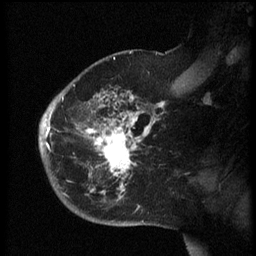
Breast MRI (dynamic contrast-enhanced), one sagittal slice; slice 42 of 60 in the series (ordered by position); dynamic contrast-enhanced series, image 2 of 3 at this slice position (ordered by acquisition); 1.5 T; TE 4.2 ms, TR 8.4 ms; 256 × 256 image matrix, field of view 200 × 200 mm. Patient: female, 38 years. From the clinical record (not read from this slice): setting: breast cancer imaged before/during neoadjuvant chemotherapy; receptor status: HER2-positive.
Annotated regions visible in this slice (semi-automatic segmentation, software-assisted and operator-edited):
- analysis volume of interest (the breast-tissue region the enhancement analysis was run in; not a lesion): bounding box <40,74,173,202> (left, top, right, bottom; pixels)
- tumour enhancement mask (voxels above the 70 % enhancement threshold inside the analysis volume of interest): <41,92,164,199>